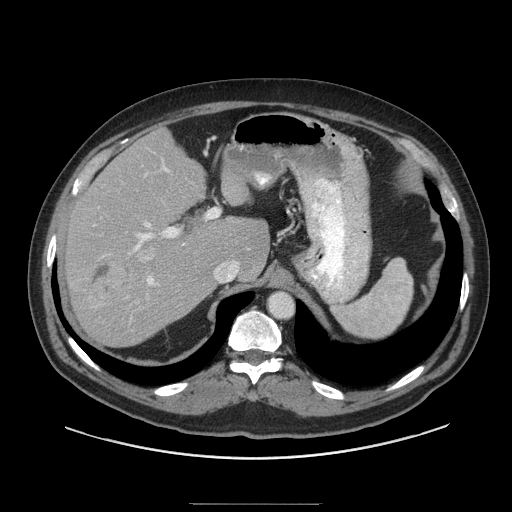
Contrast-enhanced abdominal CT (liver protocol), one axial slice; slice 67 of 91 in the series (ordered by position); soft-tissue window (W 400 / L 40 HU); 2.5 mm slice thickness; 512 × 512 image matrix. From the clinical record (not read from this slice): diagnosis: hepatocellular carcinoma (patient treated with transarterial chemoembolisation; whether this scan precedes or follows treatment is not stated here); TNM stage (as recorded): Stage-I; Child-Pugh class: A; tumour nodularity: uninodular.
Structures marked on this image (semi-automatic segmentation, software-assisted and operator-edited):
- abdominal aorta: bounding box (x1, y1, x2, y2) in pixels: (270, 293, 293, 317)
- liver parenchyma outside the tumour (the mass and vessels are separate outlines, so this box may not span the whole liver): (64, 128, 268, 346)
- mass: (89, 256, 136, 300)
- liver vessels: (103, 166, 217, 286)